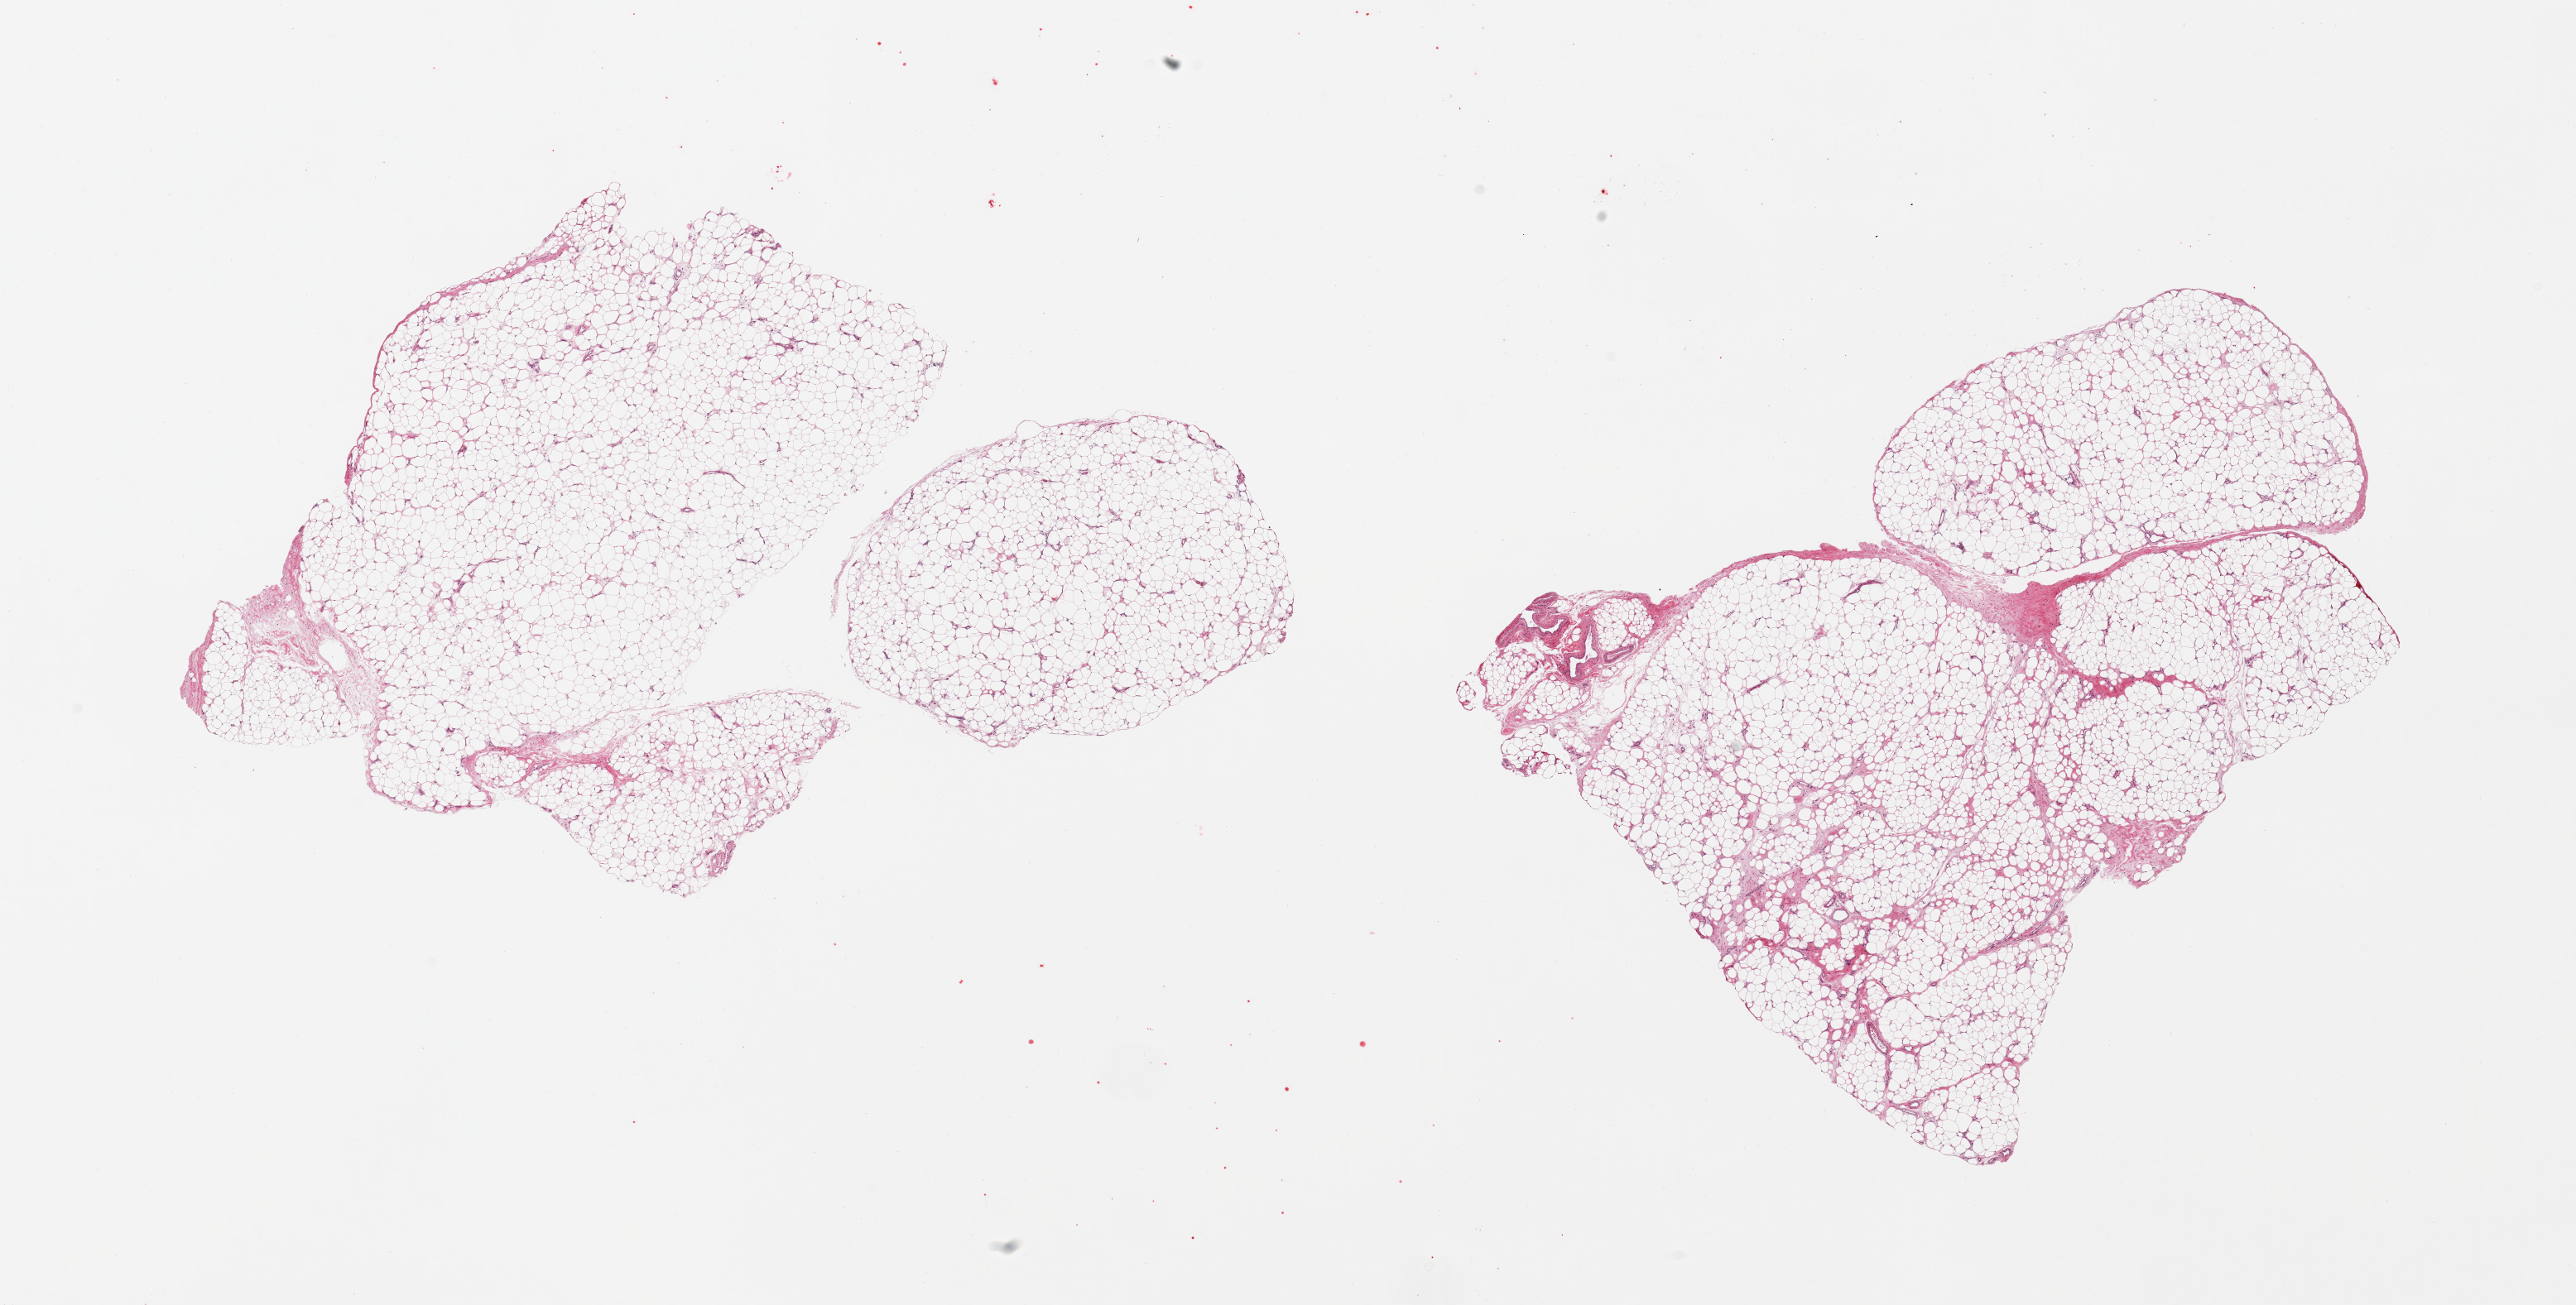
Digitized hematoxylin and eosin (H&E)-stained section, brightfield — a low-resolution overview of the entire scanned area, about 24.6 x 12.5 mm (from a 20x scan), PAXgene-fixed paraffin-embedded (PFPE) section, target tissue: adipose tissue, donor tissue sample. Donor: female.
* reviewer comment on this tissue sample: 2 pieces; mature adipose tissue